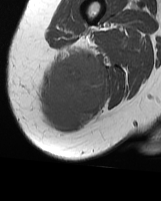
MRI of an extremity soft-tissue mass, one axial slice; position 18 of 70 along the scan axis; MR volume resampled by the dataset authors to the PET/CT grid (not the native acquisition matrix); 3.27 mm slice thickness; 161 × 201 image matrix, field of view 157 × 196 mm. Female patient. Case-level facts recorded for this patient, not image findings: histological type: synovial sarcoma; grade: intermediate; site of the primary tumour: right buttock.
Structures marked on this image (expert contour drawn on MRI and transferred to this co-registered scan by the dataset authors):
- gross tumour volume including surrounding oedema: box from (x=38, y=47) to (x=105, y=132) px
- gross tumour volume (mass): (x=42, y=52)–(x=105, y=132)